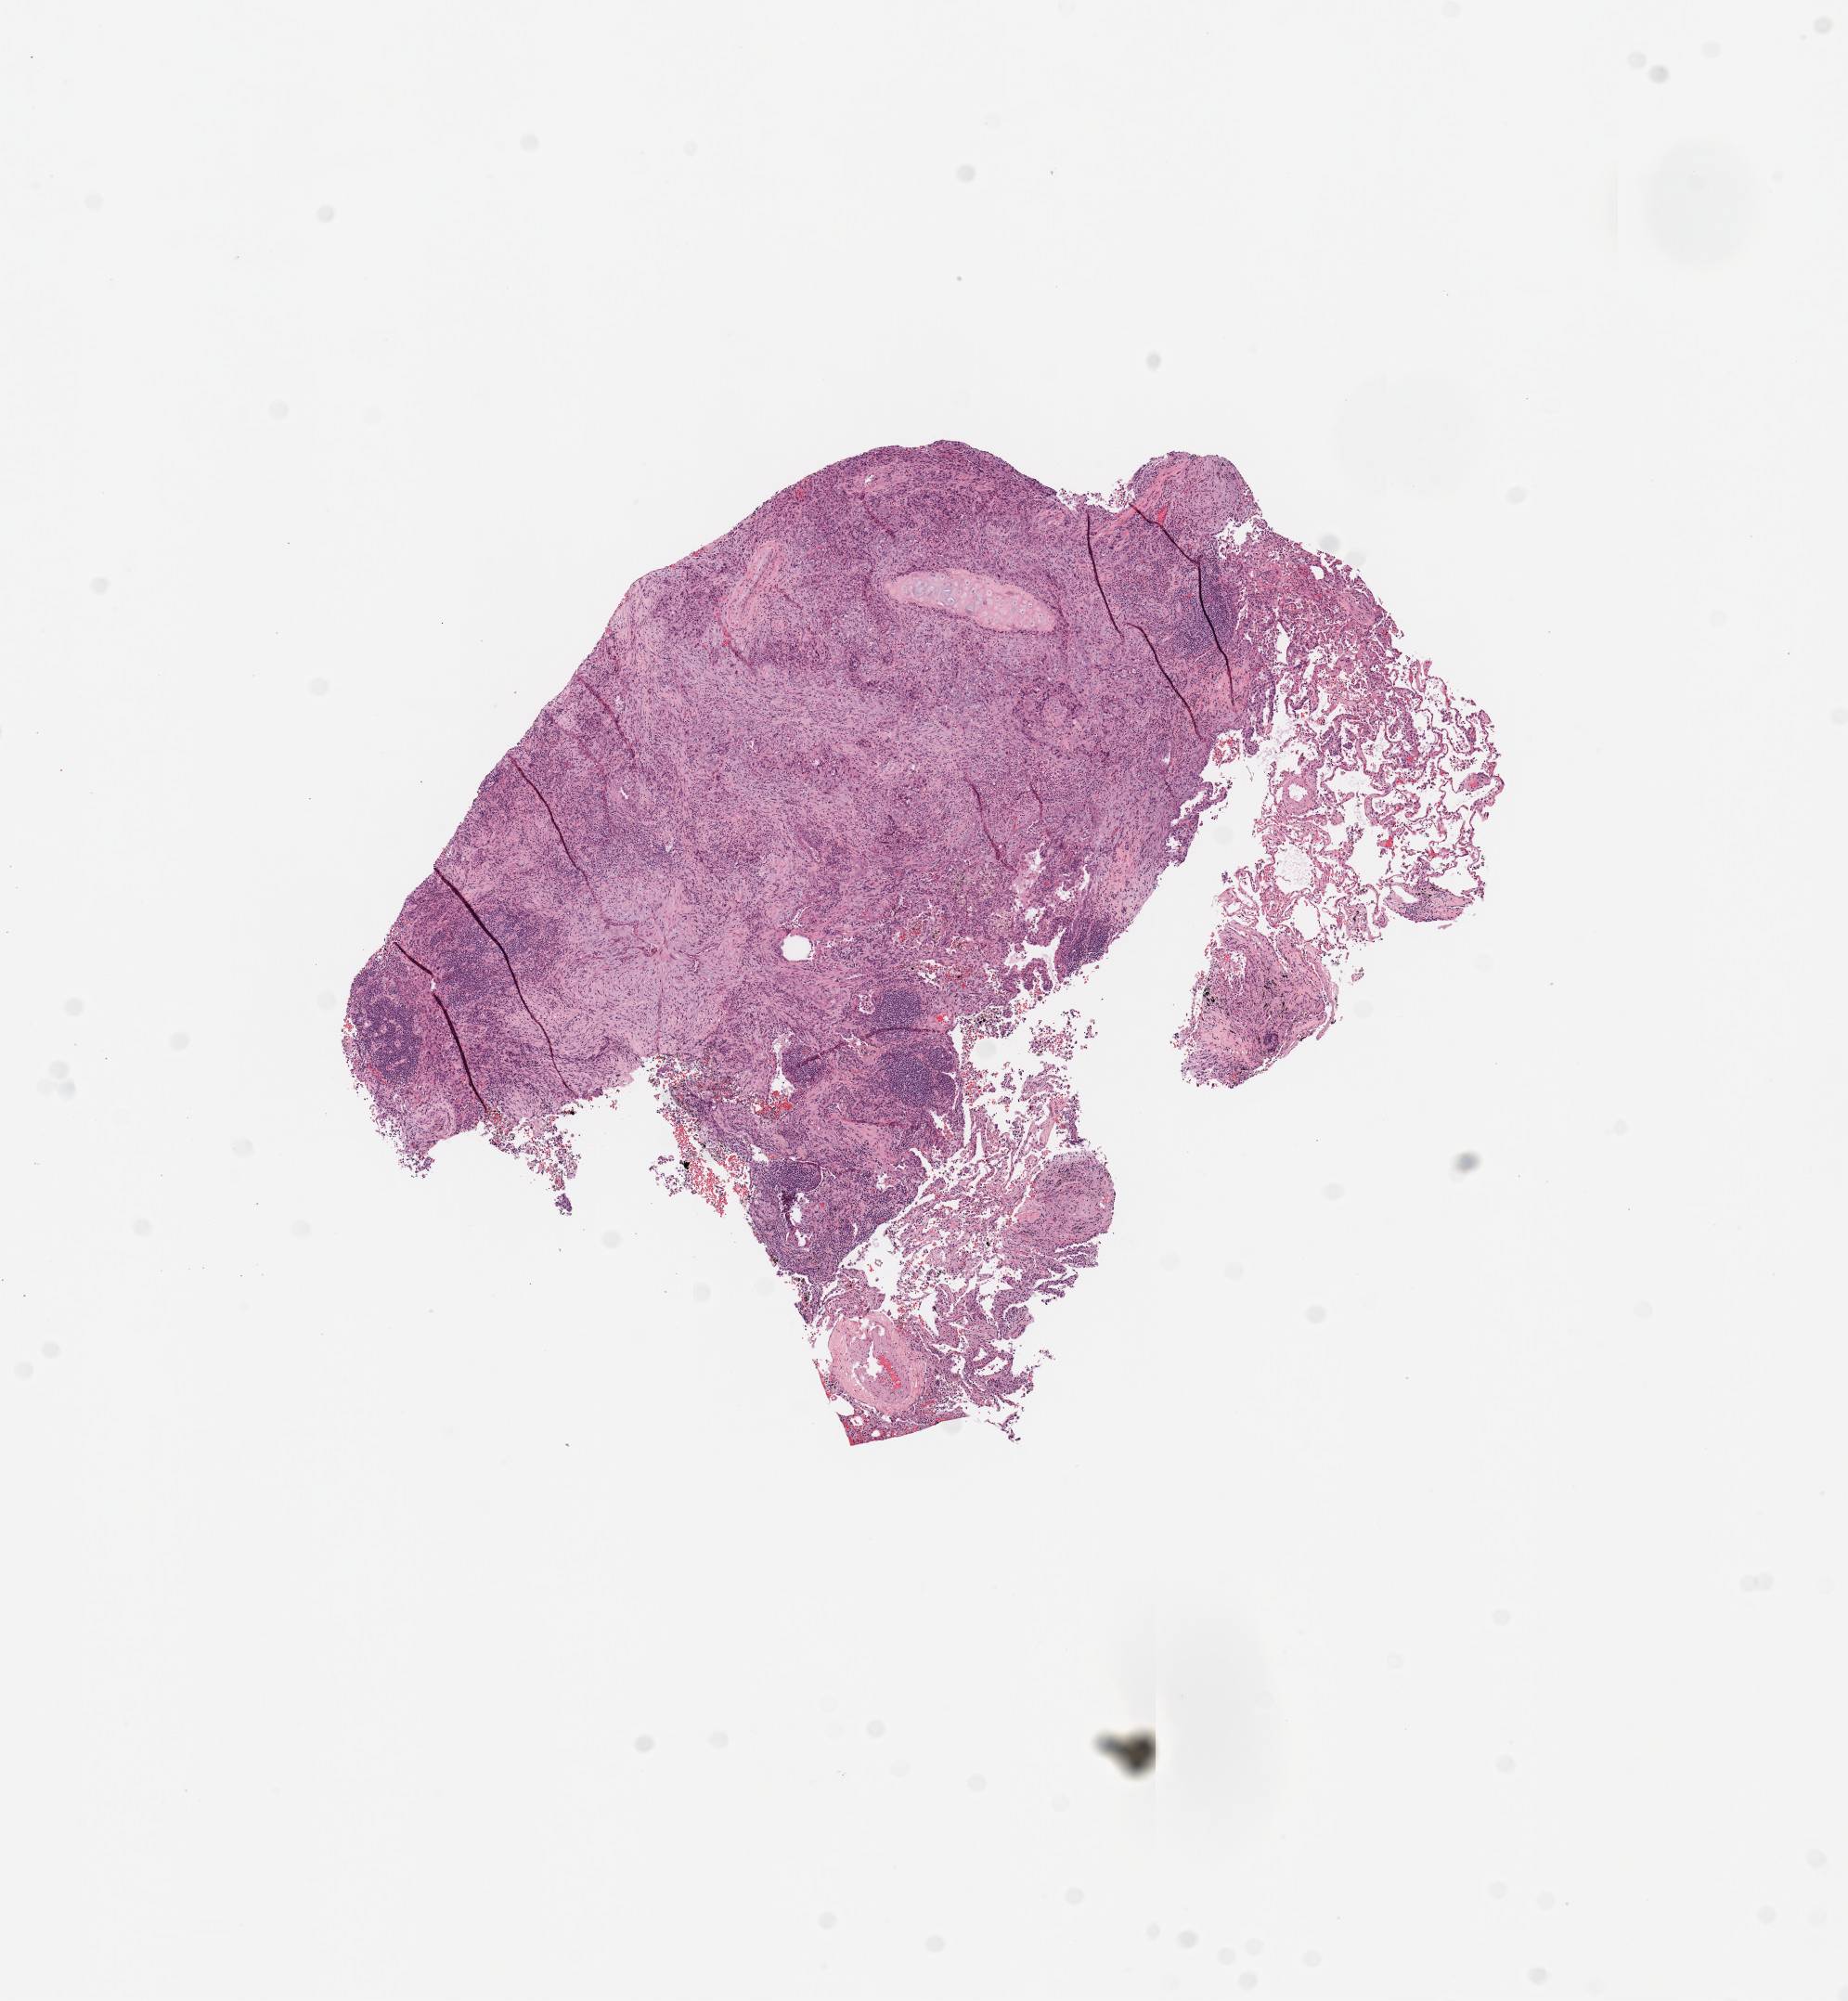
Whole-slide histology image, Hematoxylin and eosin (H&E) stained — shown as a low-resolution overview of the whole scanned area (about 7.9 x 8.5 mm, from a 20x scan); tumour tissue sample, sampled site: lung. Male, 69 y/o. Histologic grade: G3 (poorly differentiated). Slide review estimates, as recorded: tumour nuclei 50%, necrosis 0%.
AJCC pathologic stage: IB. Histologic diagnosis: Squamous cell carcinoma, NOS. Primary tumour site (as recorded): right upper lobe.